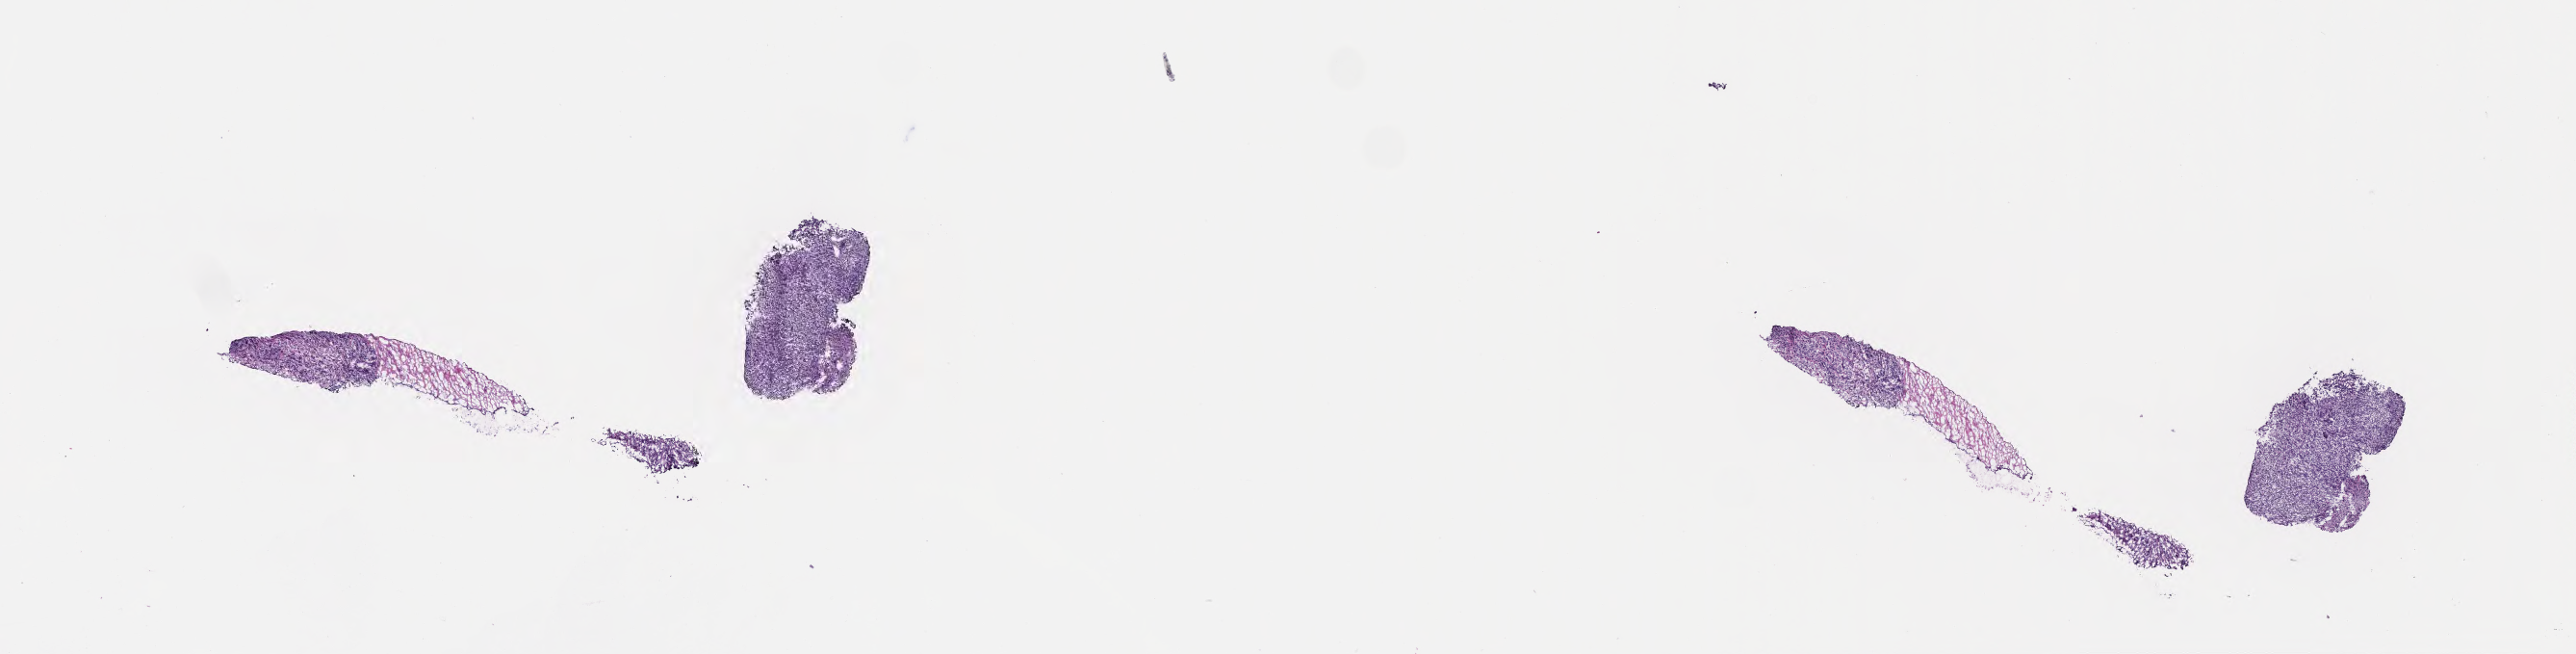
Whole-slide image, H&E stain — a low-resolution overview of the entire scanned area, about 21.6 x 5.5 mm, frozen section (tissue freezing medium), primary tumor. Patient male; 10 years old. Slide review estimates, as recorded: tumor cells 80%, tumor nuclei 90%, stromal cells 15%, necrosis 5%, normal cells 0%. Inflammatory infiltration, as recorded: lymphocyte infiltration 10%, monocyte infiltration 30%, neutrophil infiltration 5%.
• diagnosis: Burkitt lymphoma, NOS
• Ann Arbor stage (patient): Stage III